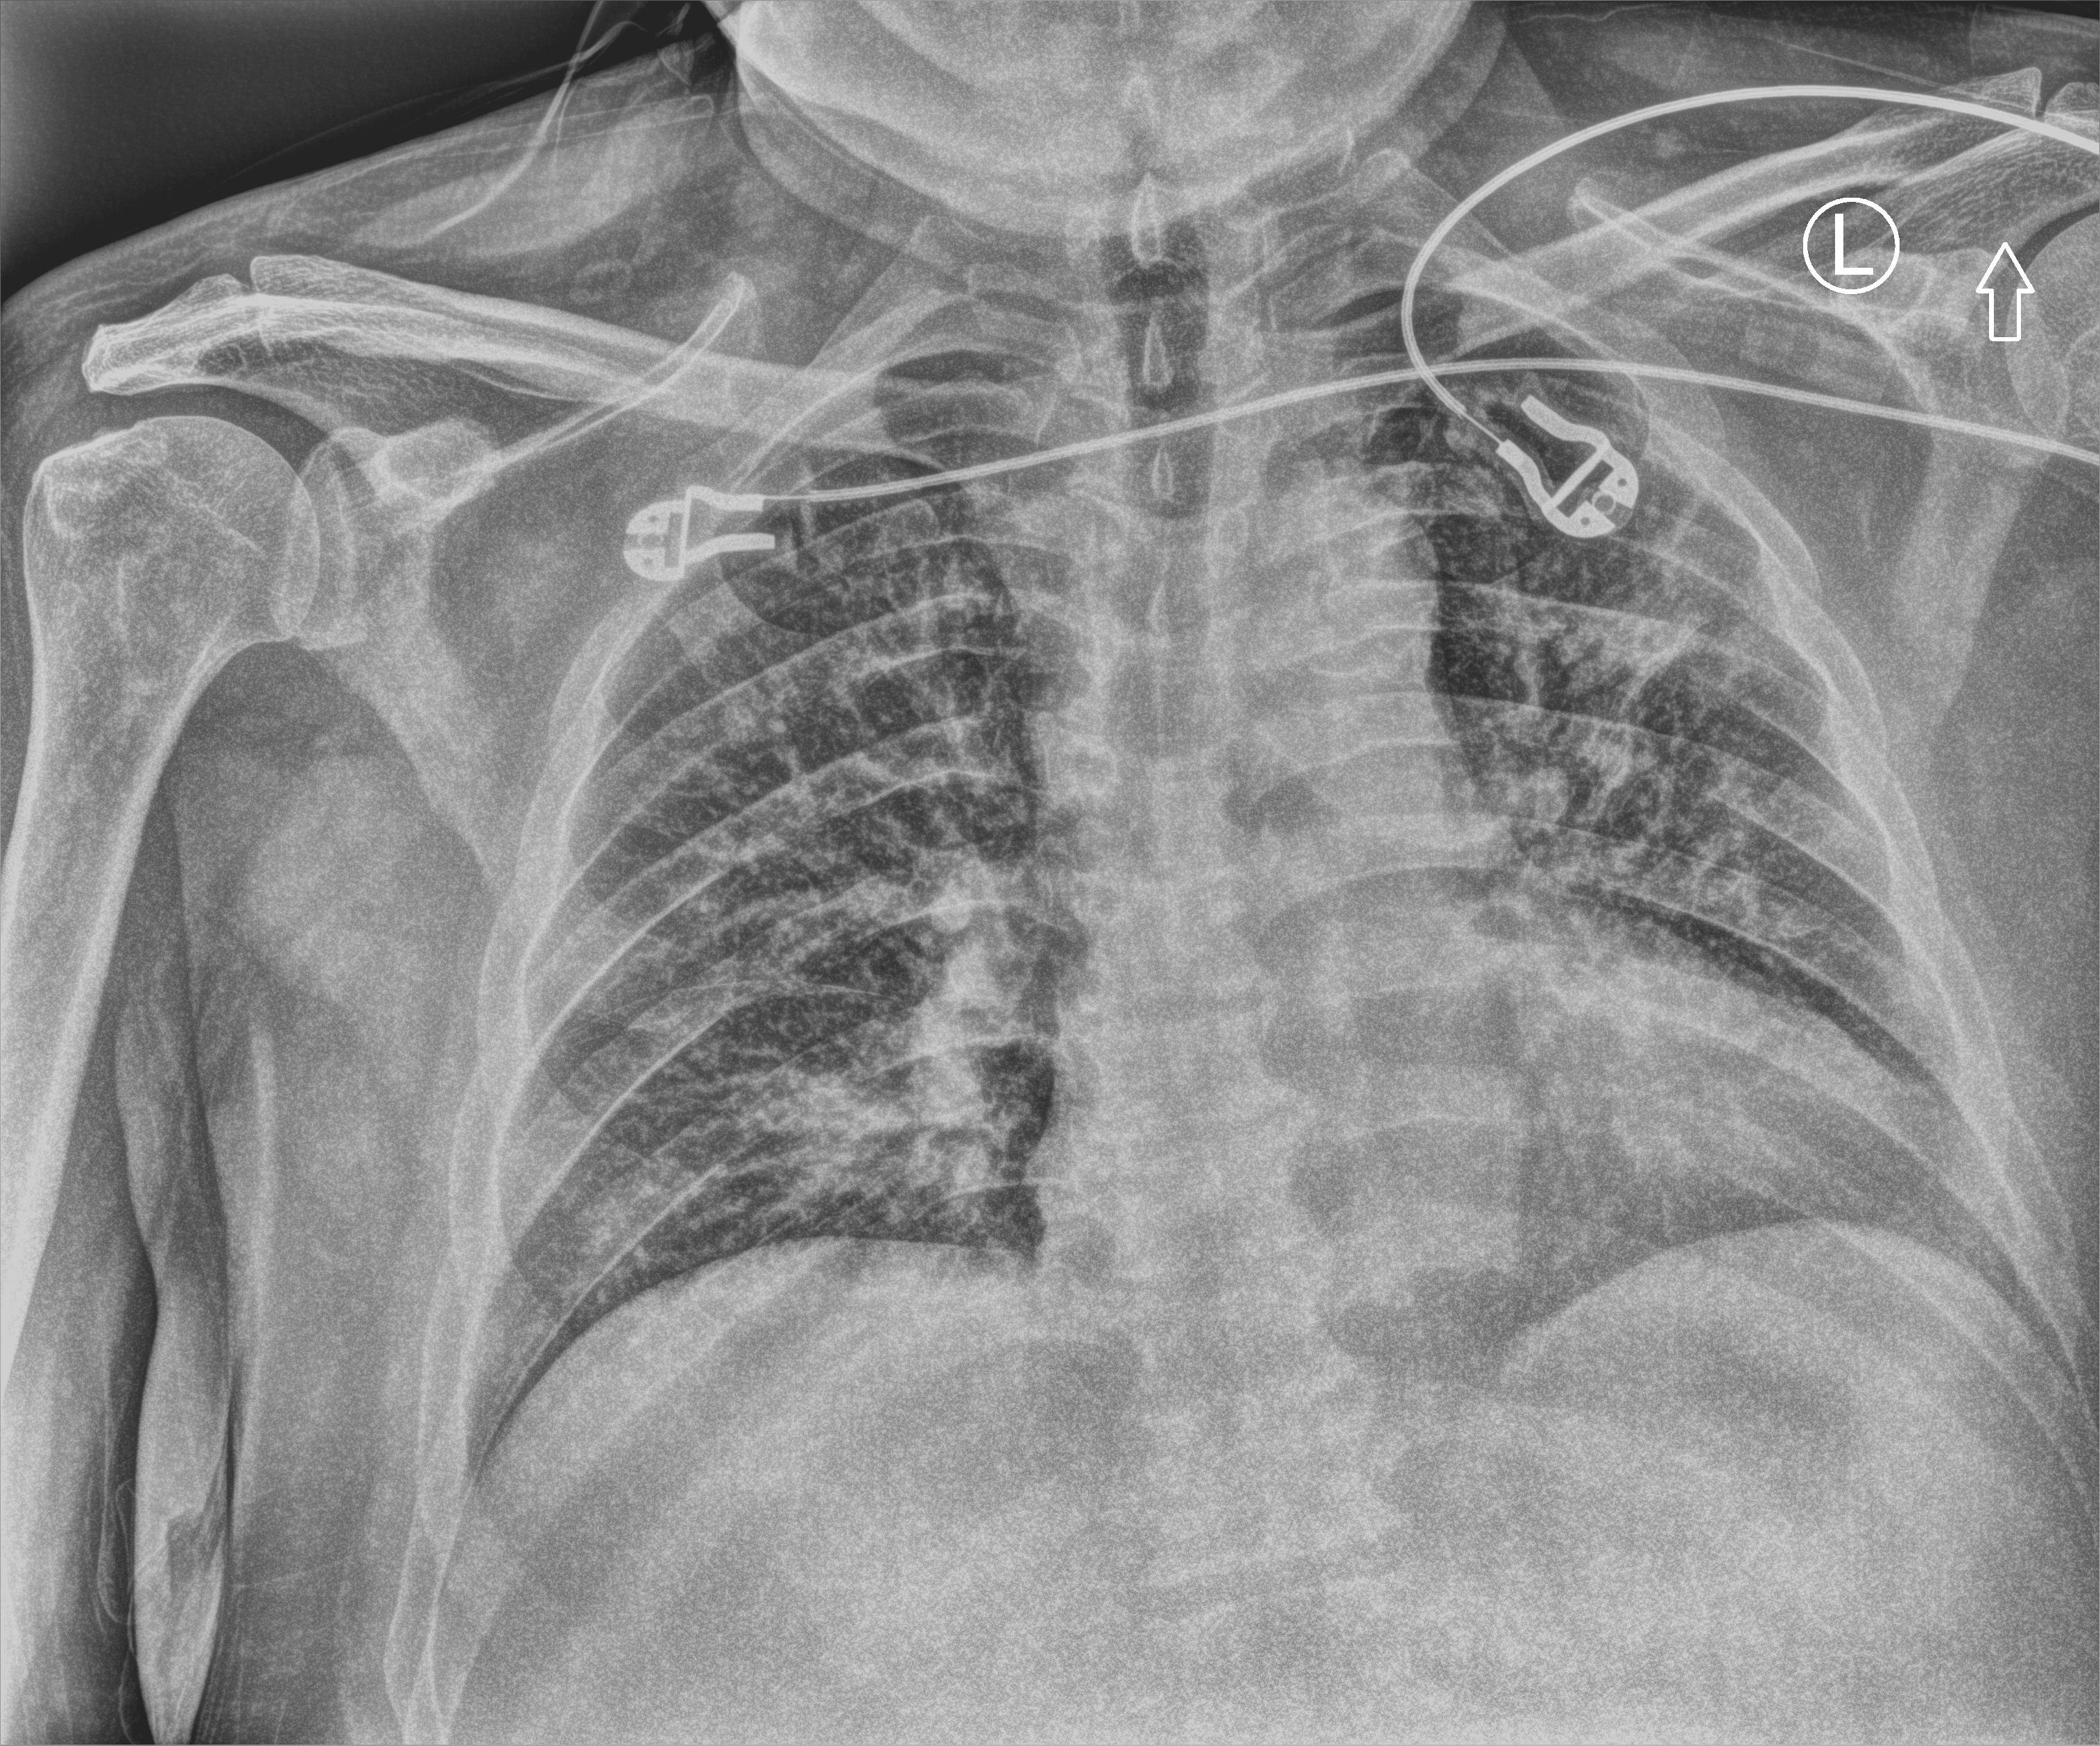
Bedside chest radiograph (computed radiography); anteroposterior (AP) projection. Patient hospitalised with COVID-19; male, aged 18–59 years.
From the hospital-stay record, not from the radiograph (when in the stay this image was taken is not recorded): admitted to intensive care during this hospital stay: no; length of hospital stay: 18 days; mechanically ventilated during this hospital stay: no.